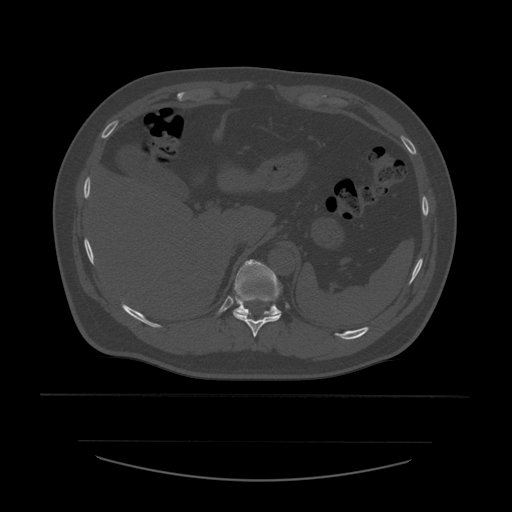
CT including the spine, one axial slice; 120 kVp; bone window (W 1800 / L 400 HU); 512 × 512 image matrix. Patient age 44 years. From the clinical record (not read from this slice): primary cancer: soft tissue sarcoma.
Structures marked on this image (semi-automatic segmentation, software-assisted and operator-edited):
- T10 vertebra: bounding box <234,294,282,337> (left, top, right, bottom; pixels)
- T11 vertebra: <233,259,282,317>